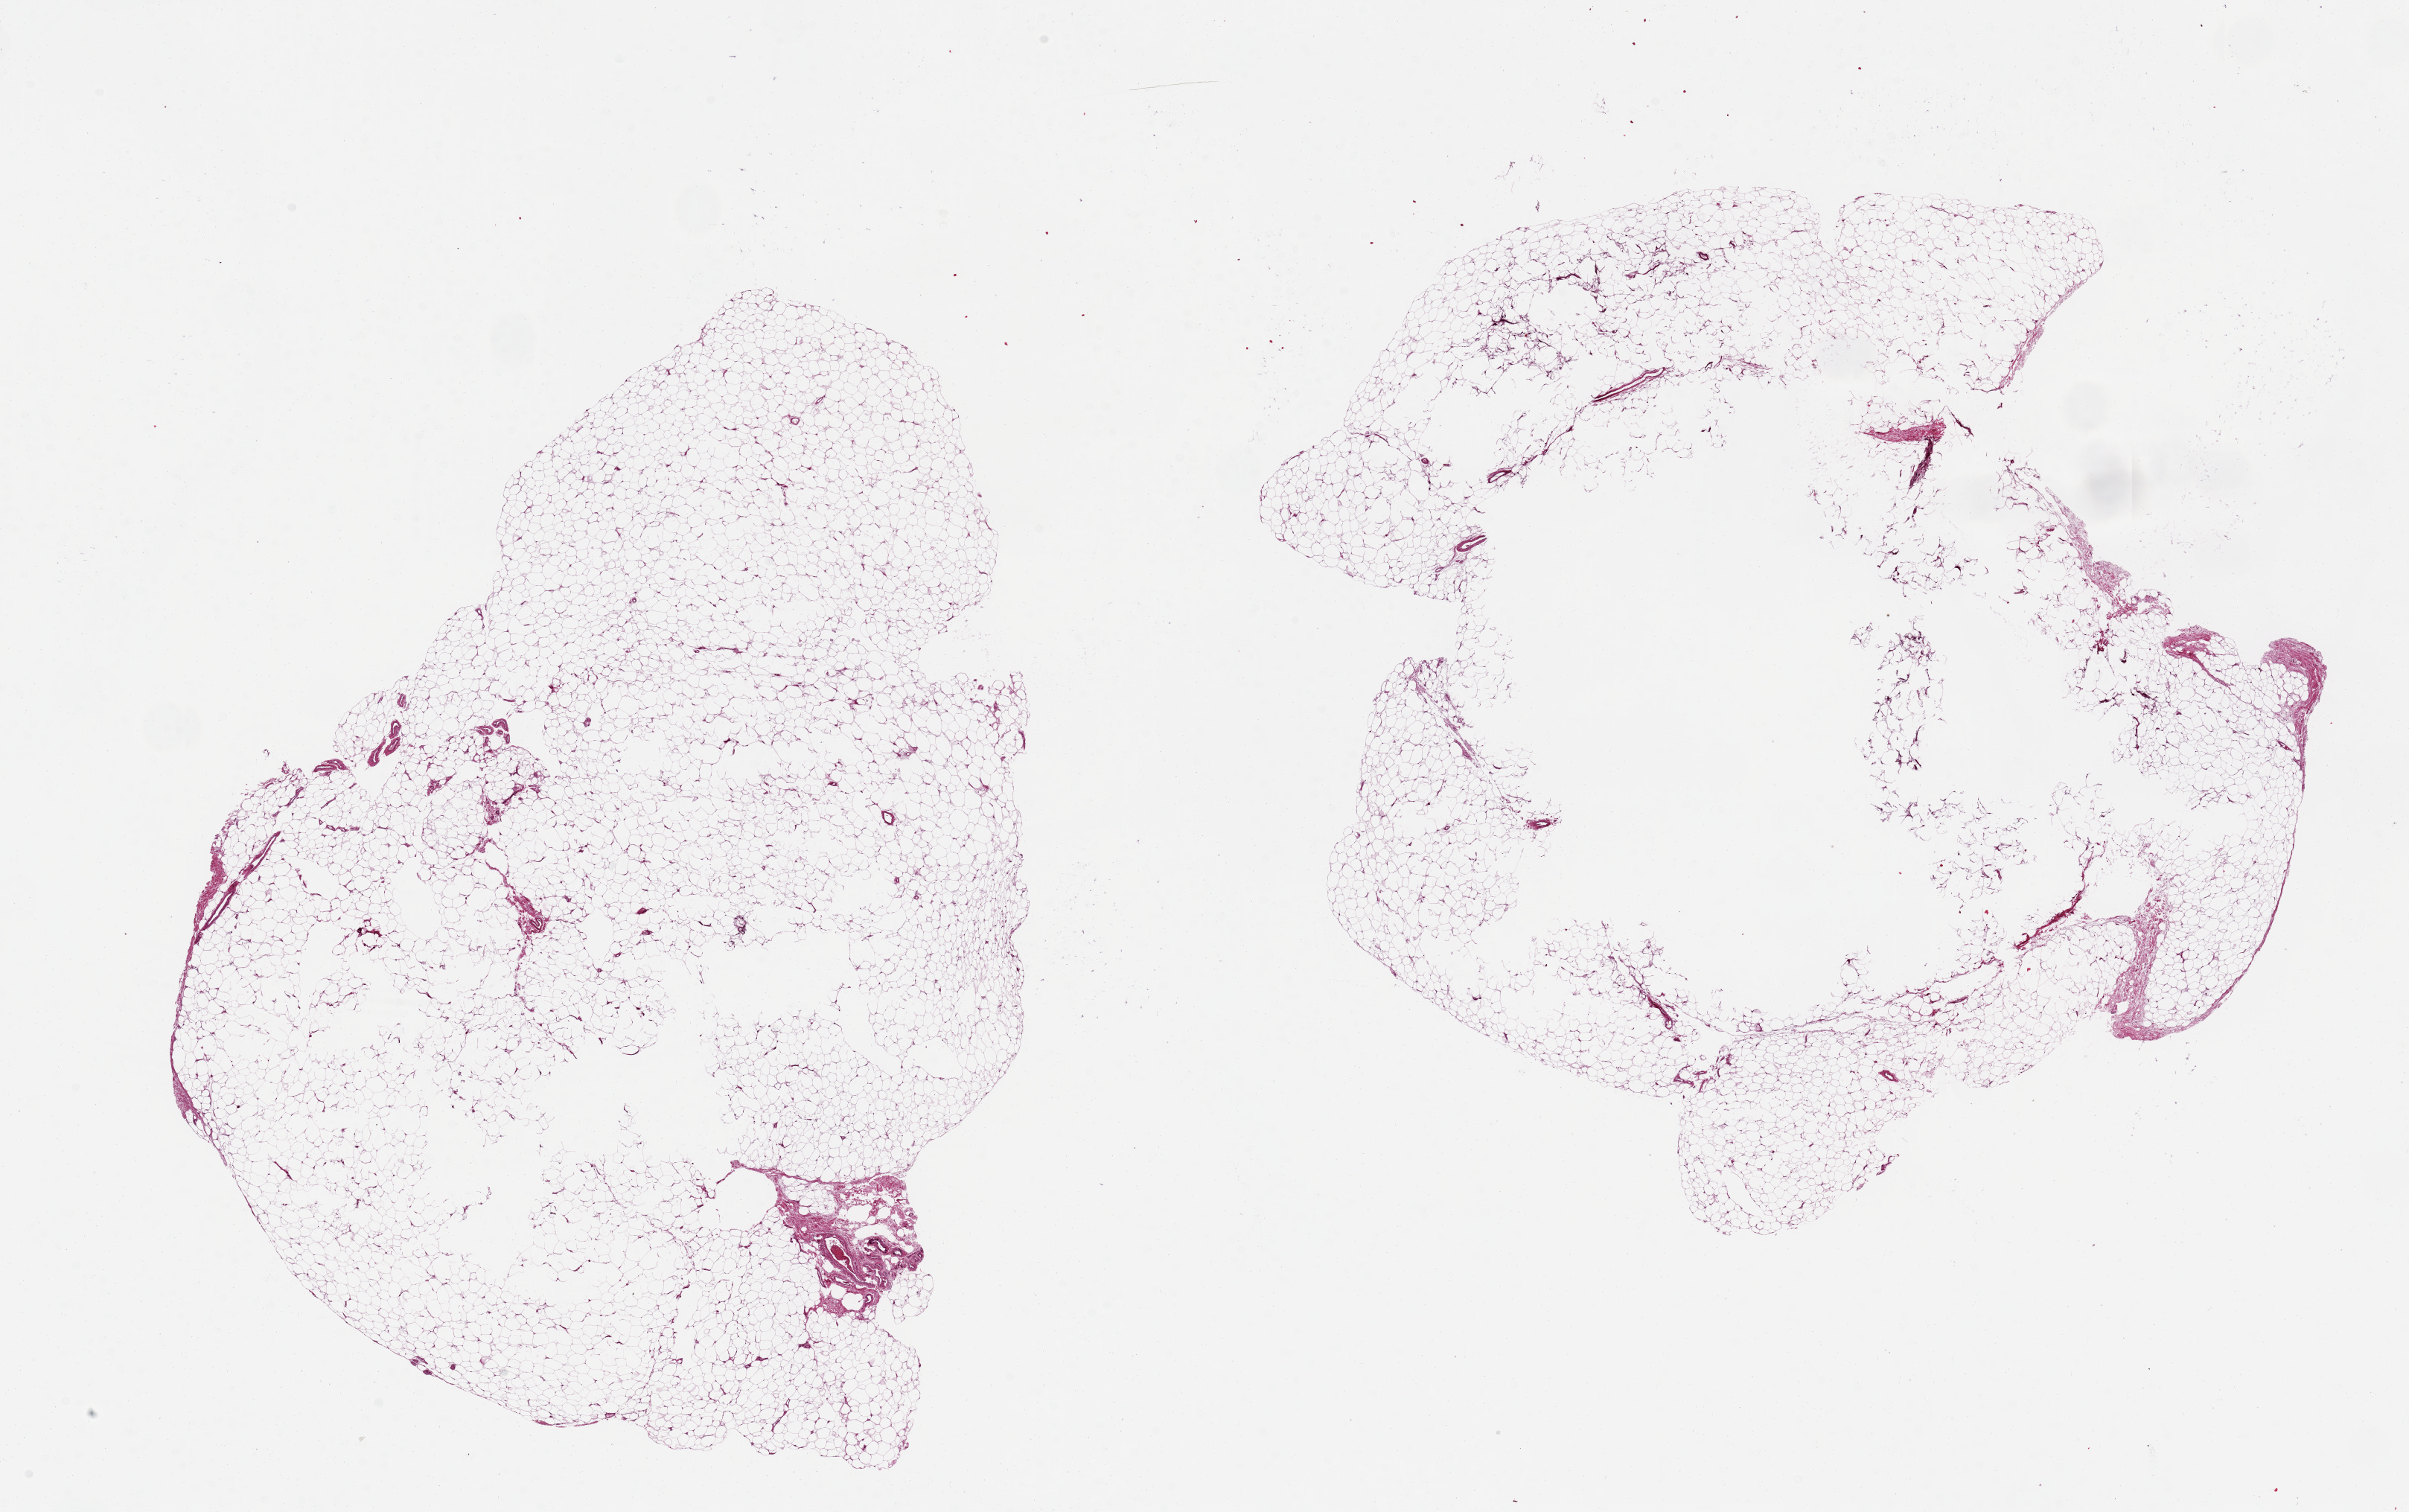
Digitized H&E-stained section — low-resolution overview of the scanned area, about 25.6 x 16.1 mm; PAXgene-fixed paraffin-embedded (PFPE) section; sampled site (target tissue): adipose tissue; donor tissue sample. Female donor.
• reviewer comment on this tissue sample: 2 pieces, 12x9 & 11x9 mm, one with large central unfixed hole